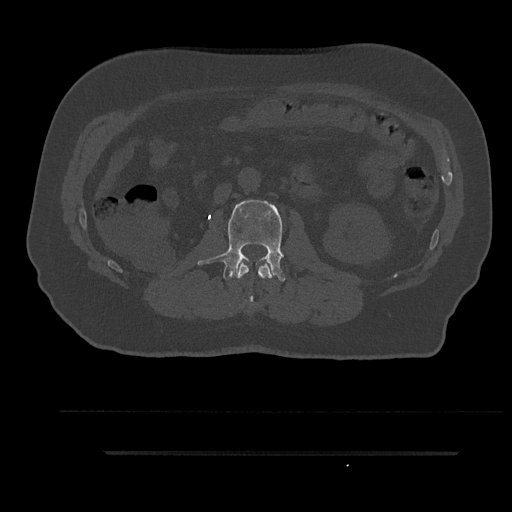
CT including the spine, one axial slice; slice 125 of 797 in the series (ordered by position); reconstruction kernel Br40s/3; 120 kVp; bone window (W 1800 / L 400 HU); 0.5 mm slice thickness; 512 × 512 image matrix, field of view 432 × 432 mm. Patient: male, 63 years. Case-level facts recorded for this patient, not image findings: primary cancer: renal.
Structures marked on this image (semi-automatic segmentation, software-assisted and operator-edited):
- L1 vertebra: bounding box [x1, y1, x2, y2] px = [236, 261, 276, 305]
- L2 vertebra: [198, 200, 285, 281]